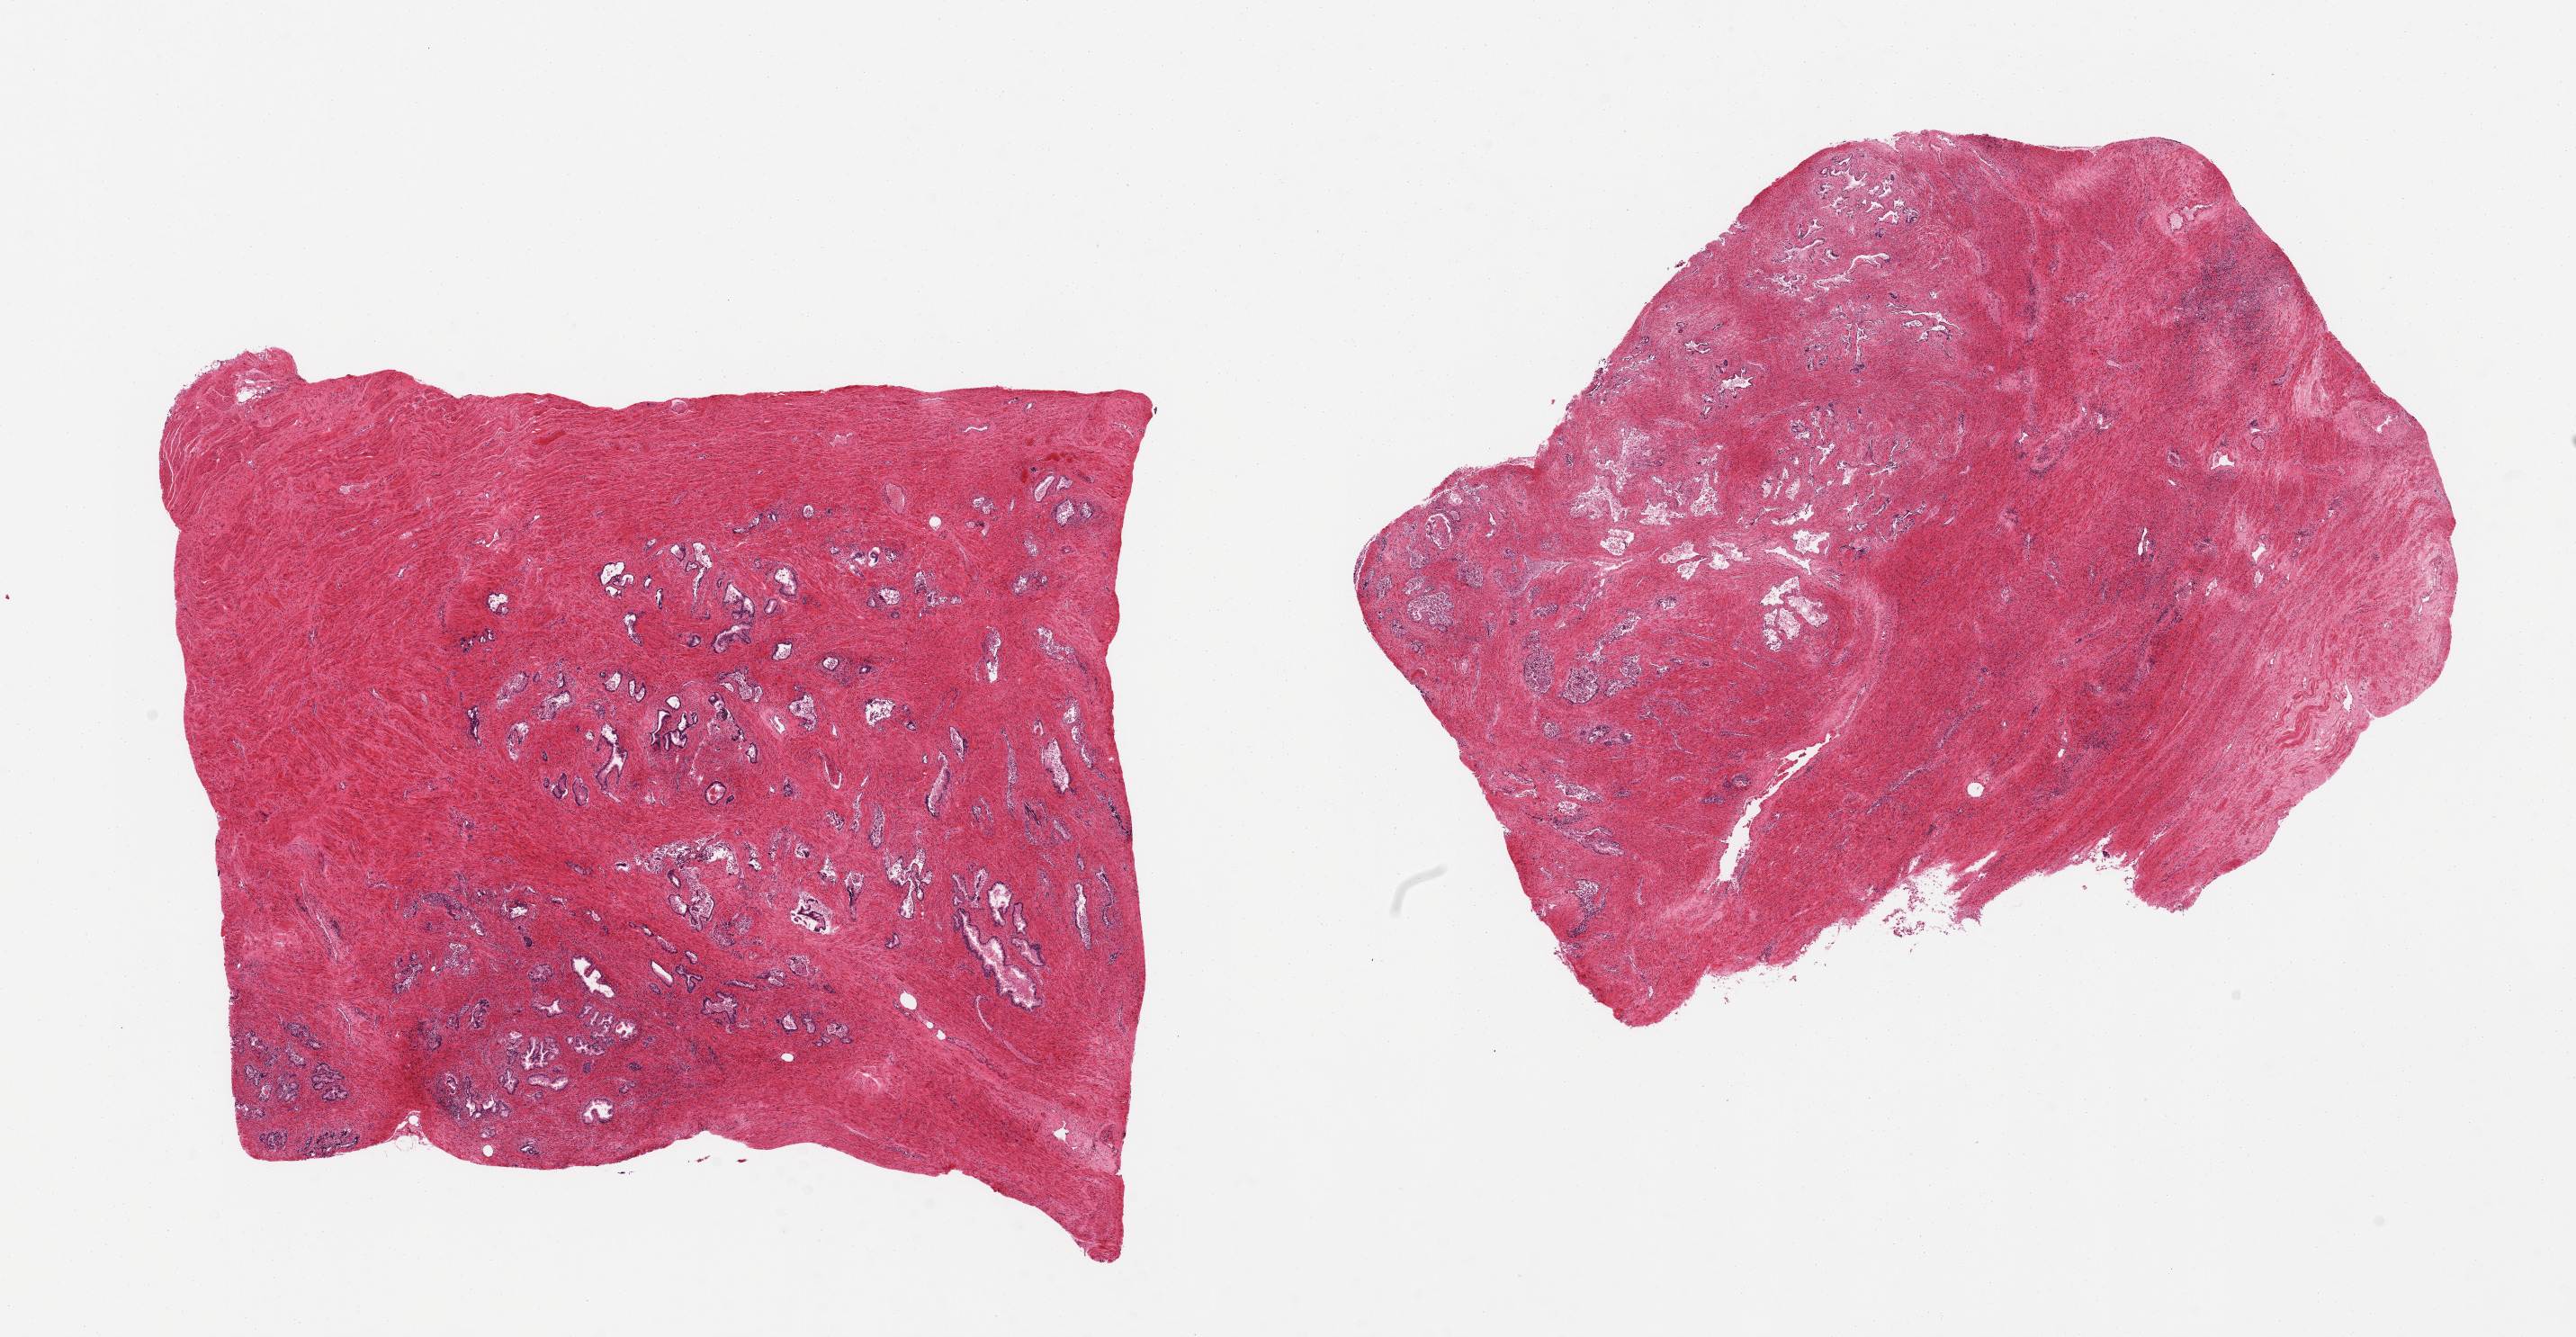
Digitized haematoxylin and eosin-stained section, brightfield, whole scanned area (about 22.6 x 11.8 mm, from a 20x scan) shown as a low-resolution overview. PAXgene-fixed paraffin-embedded (PFPE) section. Sampled site (target tissue): prostate. Donor tissue sample. Donor: male.
Review note (as recorded): 2 pieces, glandular elements moderate-severely autolyzed.